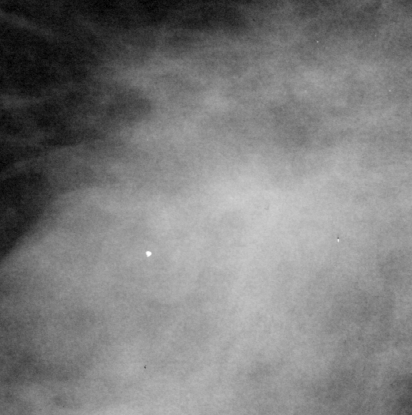
Region of interest cut from a scanned film mammogram (one marked finding); right breast; CC view; BI-RADS breast density category 3 (scale 1–4).
Finding: mass, shape irregular, margins spiculated; BI-RADS assessment category 5; pathology (as recorded): malignant.